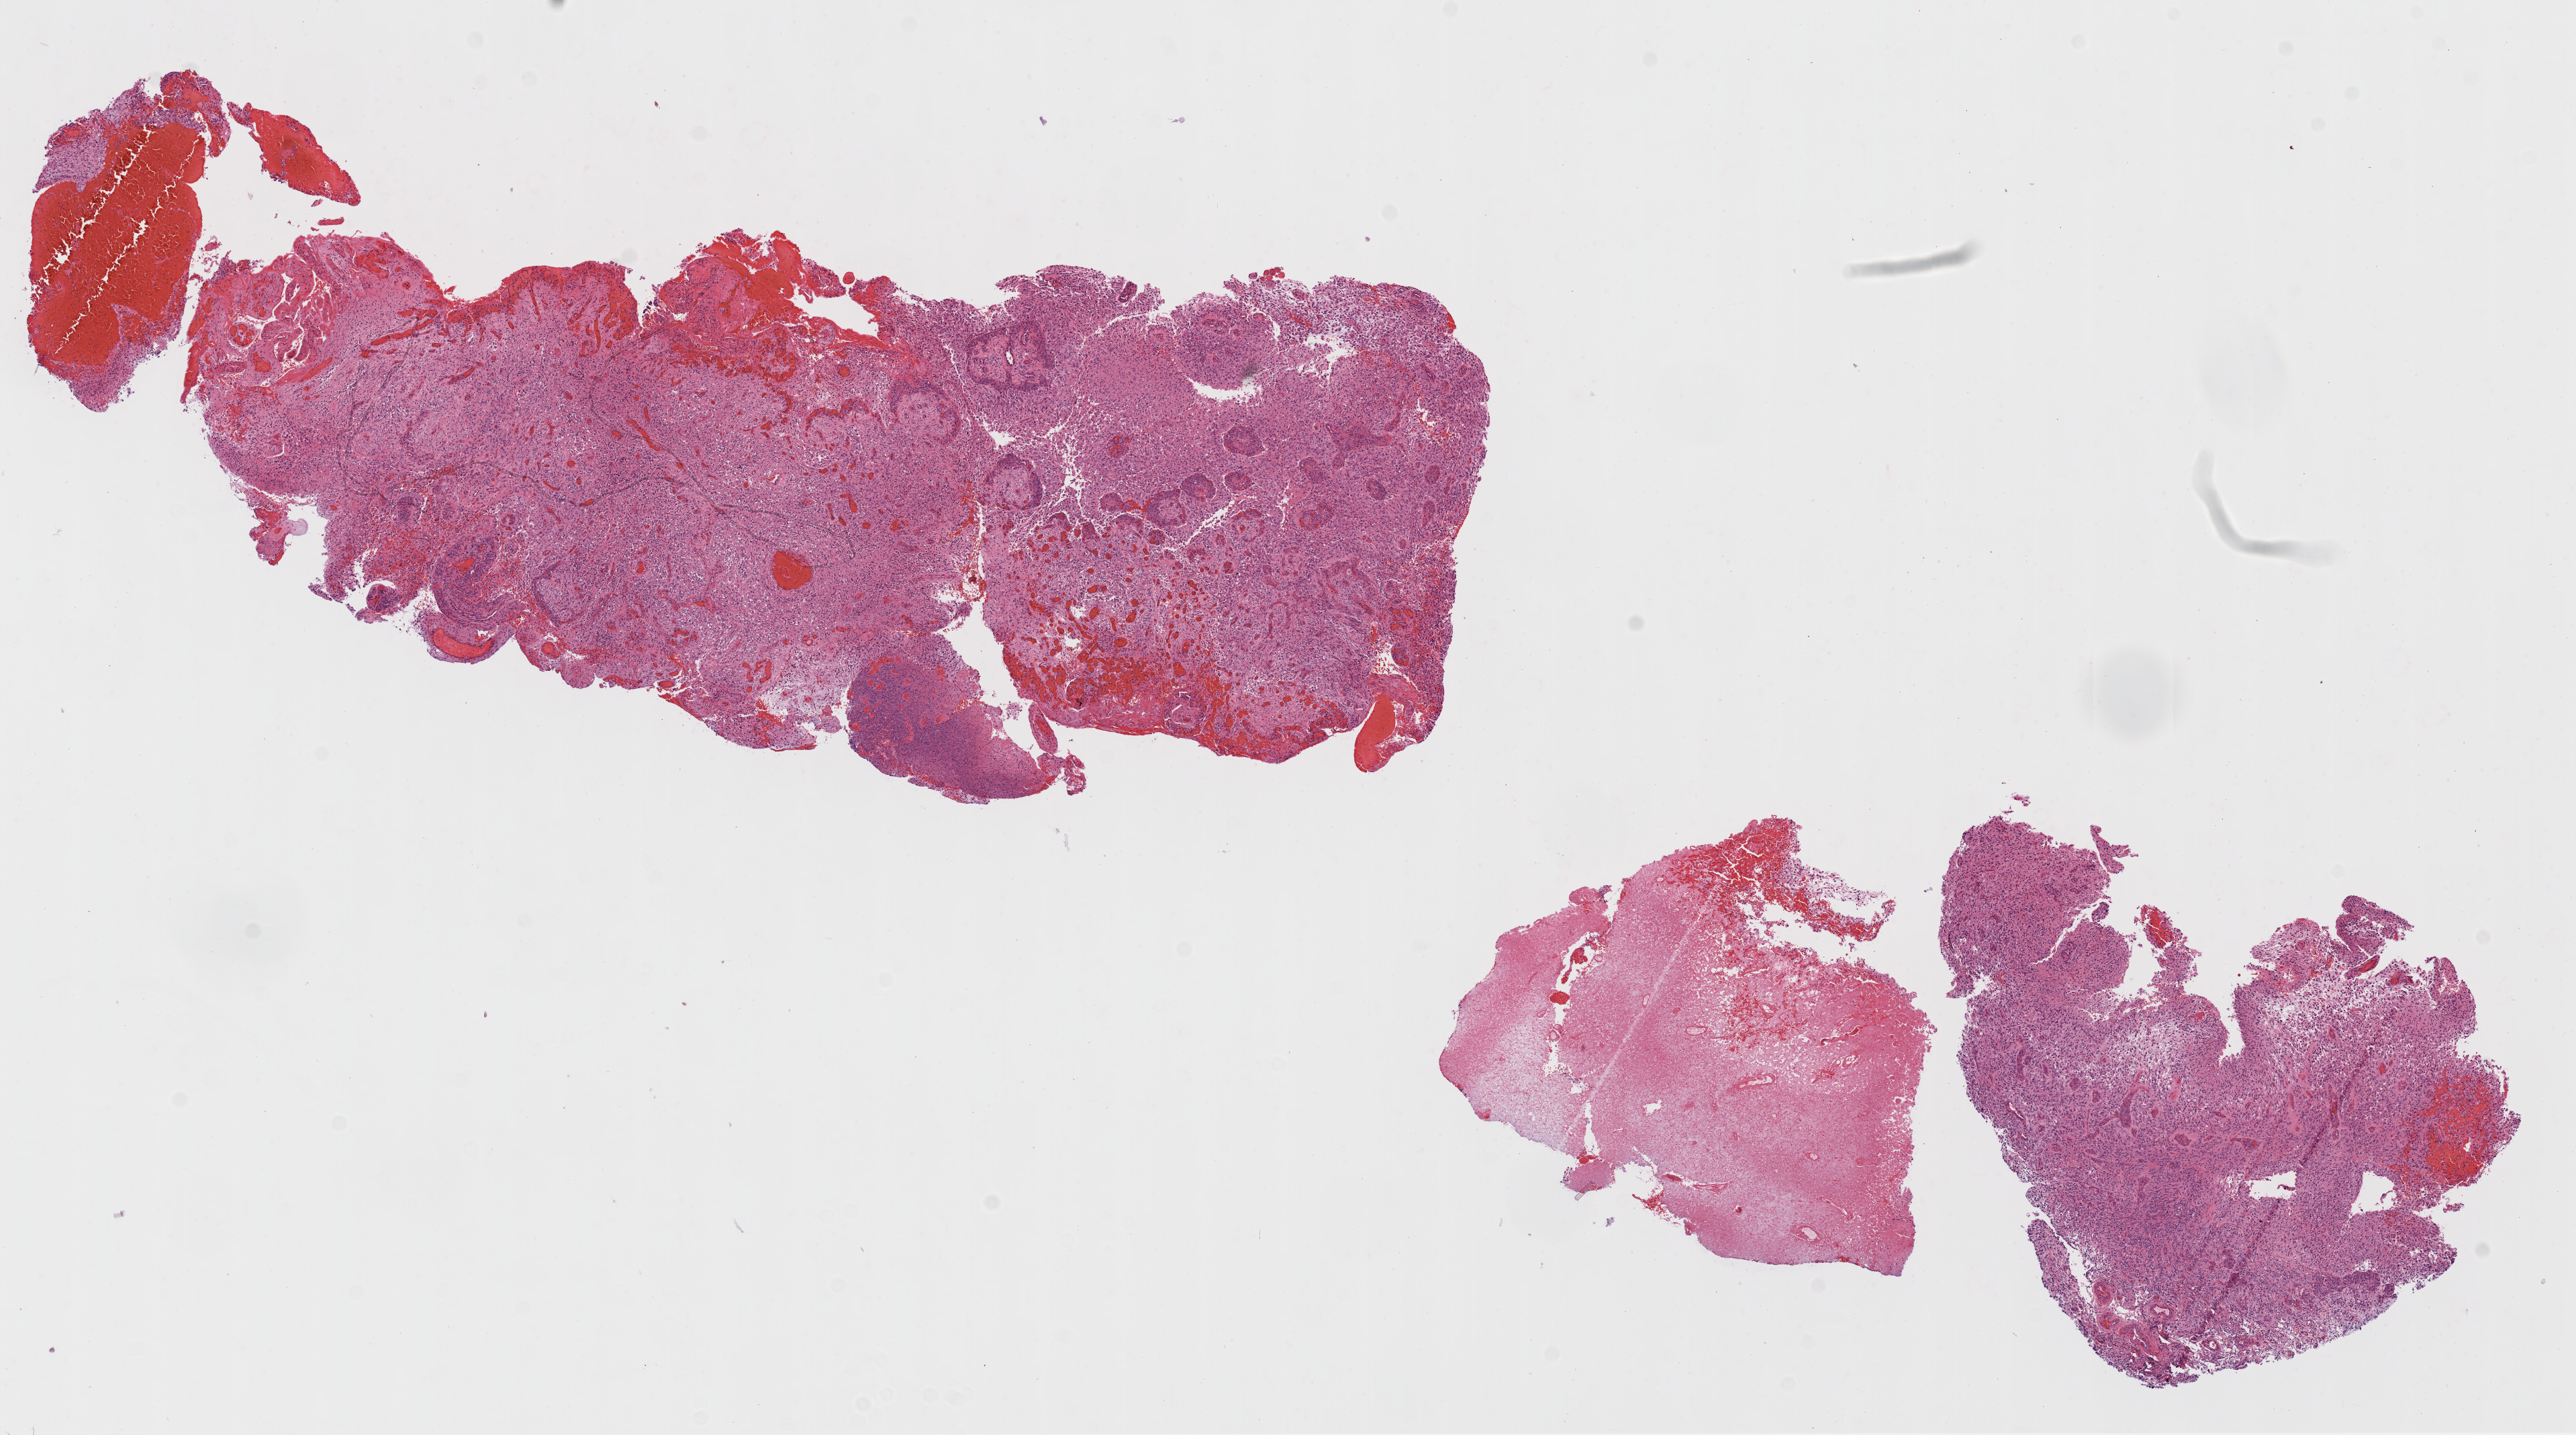
Digitized Hematoxylin and eosin (H&E) stained tissue section (whole slide) — shown as a low-resolution overview of the whole scanned area (about 15.5 x 8.6 mm), formalin-fixed paraffin-embedded (FFPE) diagnostic section, brain, primary tumour sample. Patient: male, age at initial diagnosis 67 years.
• histologic diagnosis: Glioblastoma